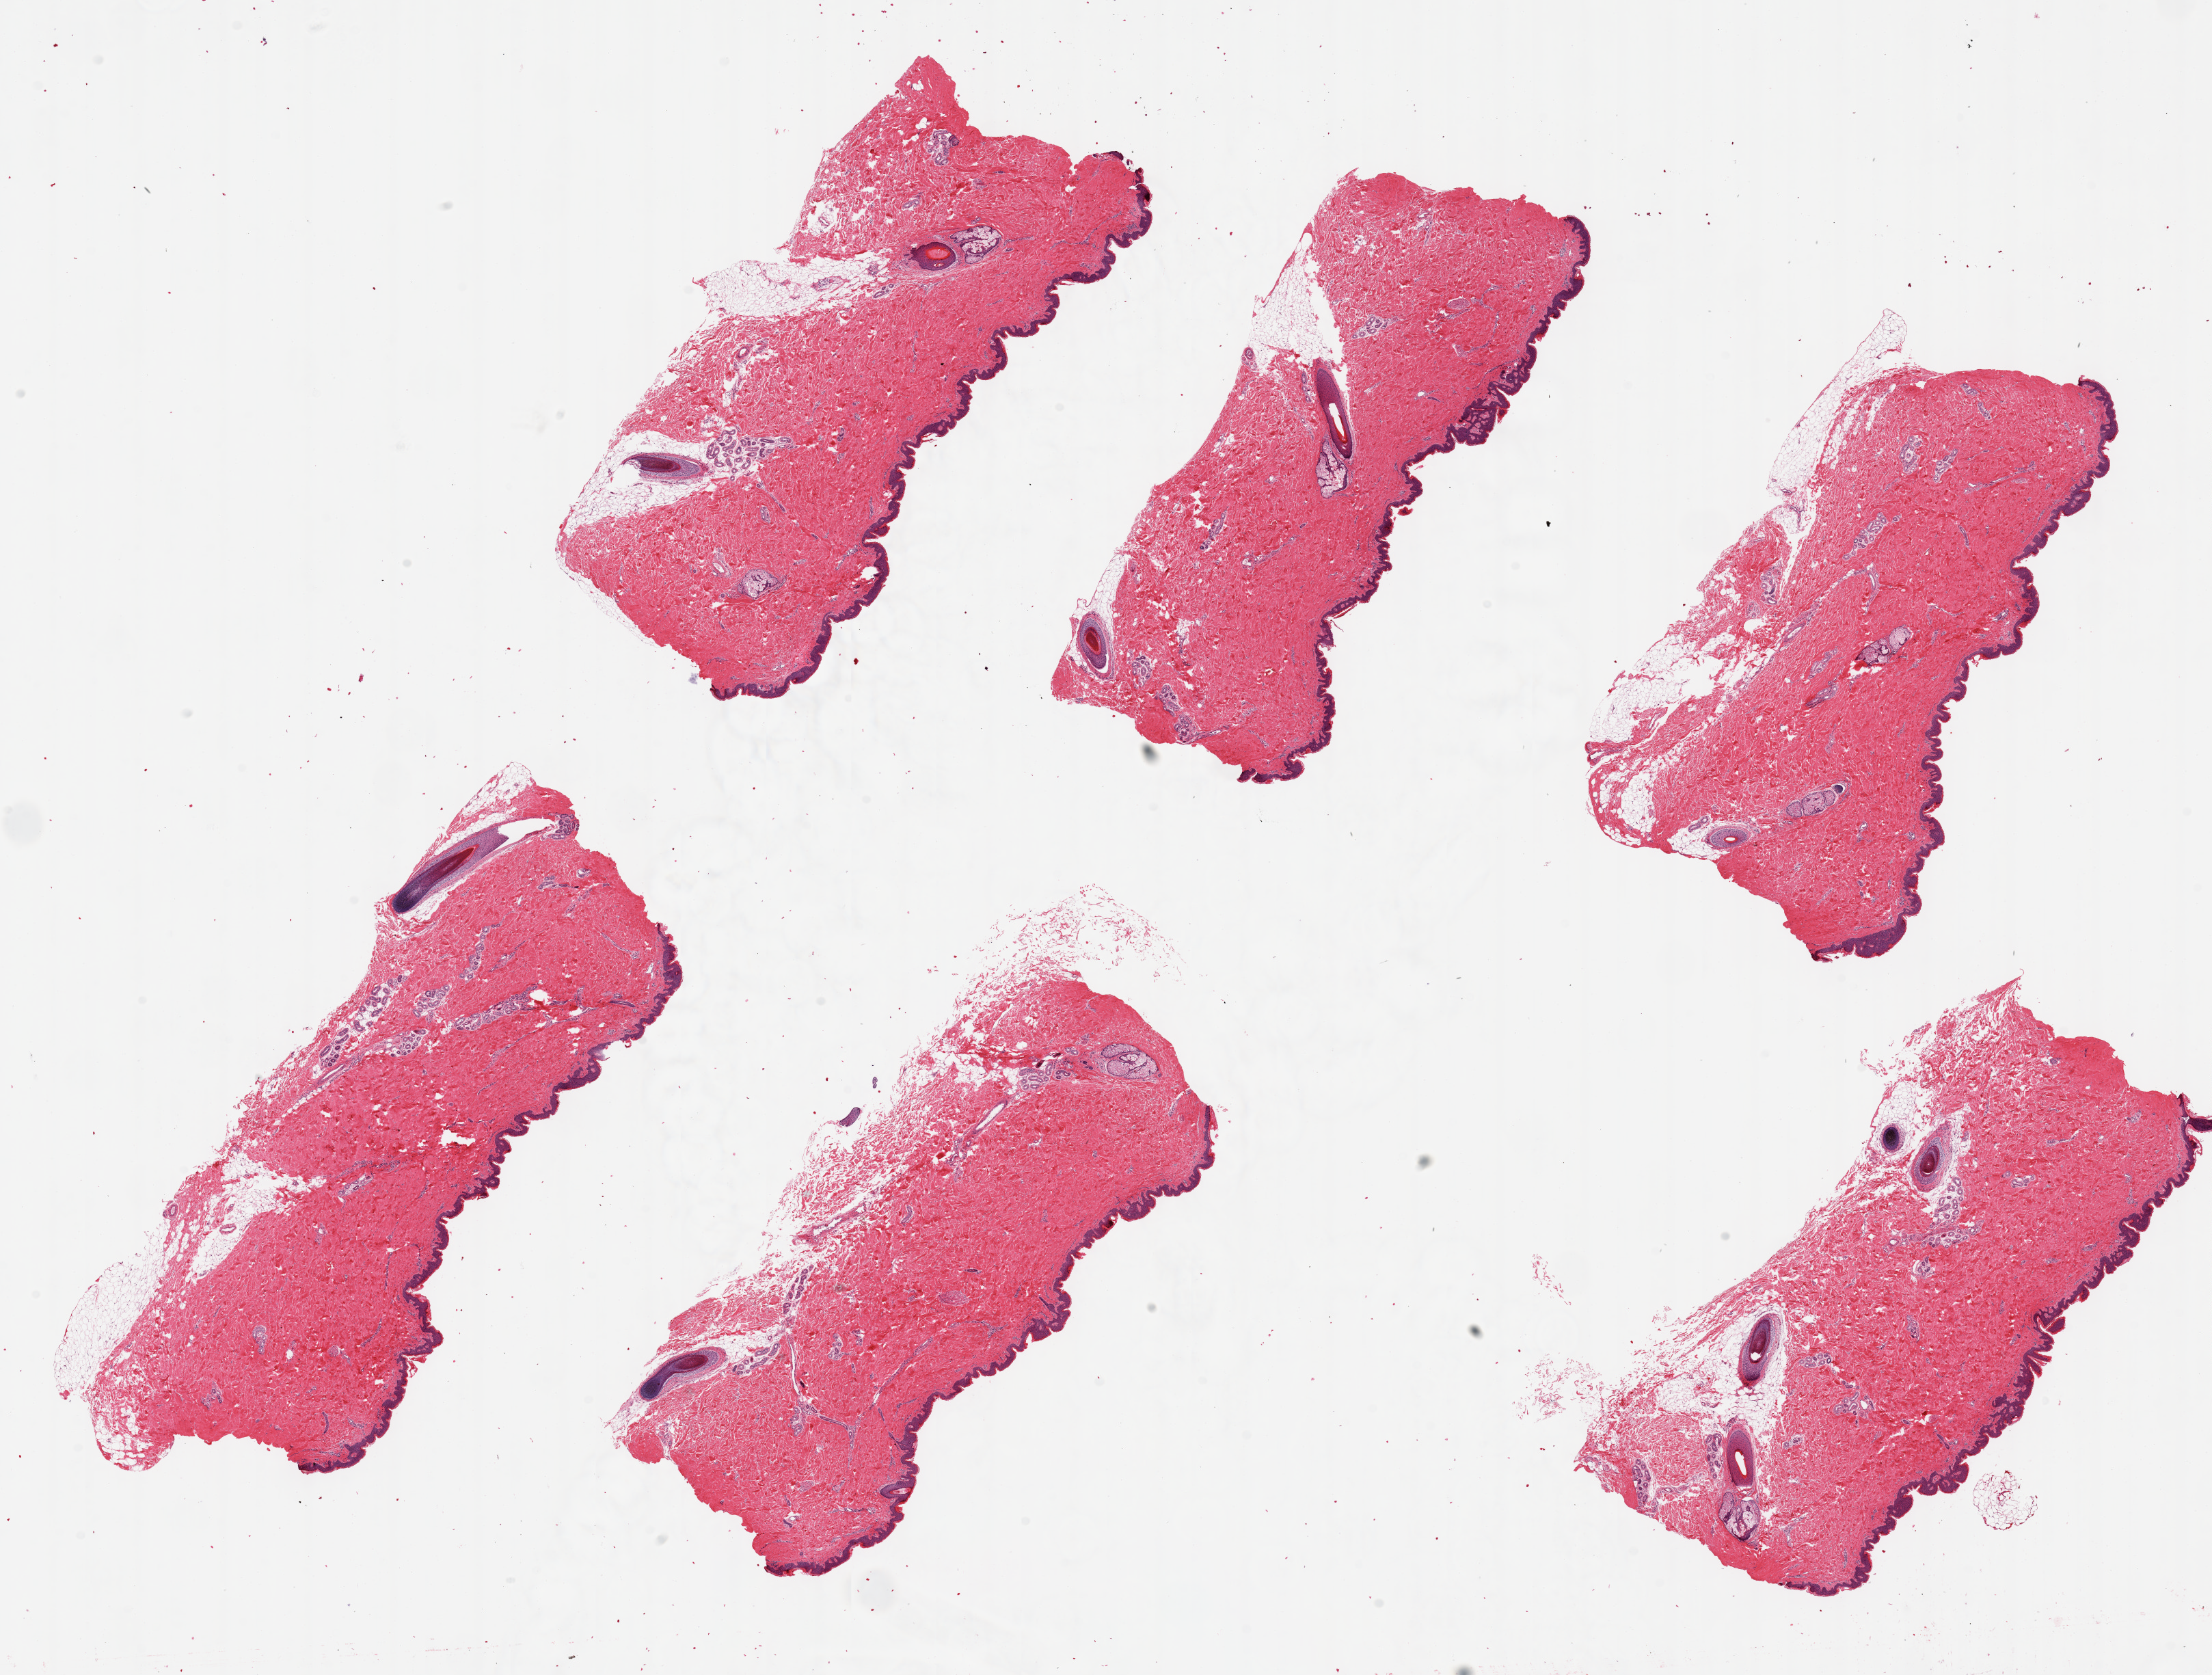
Digitized H&E-stained section — low-resolution overview of the scanned area, about 25.6 x 19.4 mm (from a 20x scan). PAXgene-fixed paraffin-embedded (PFPE) section. Section of skin of suprapubic region (target tissue). Tissue donor sample.
- reviewer comment on this tissue sample: 6 pieces ~7x3mm. Squamous epithelium is ~2-3% of thickness